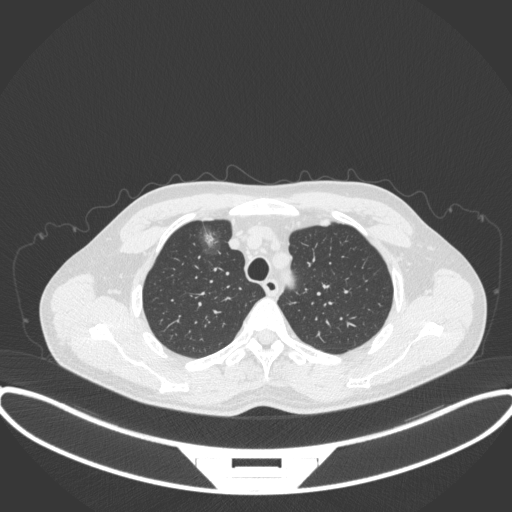
Chest CT, one axial slice; position 293 of 395 along the scan axis; 120 kVp; lung window (W 1500 / L -600 HU); 1 mm slice thickness; 512 × 512 image matrix. Patient: male, 60 years. Case-level facts recorded for this patient, not image findings: clinical TNM (as recorded): T1c N0 M0.
Structures marked on this image (rectangle marked by the reading radiologist):
- lung tumour (recorded histology: adenocarcinoma): bounding box [x1, y1, x2, y2] px = [193, 221, 223, 259]